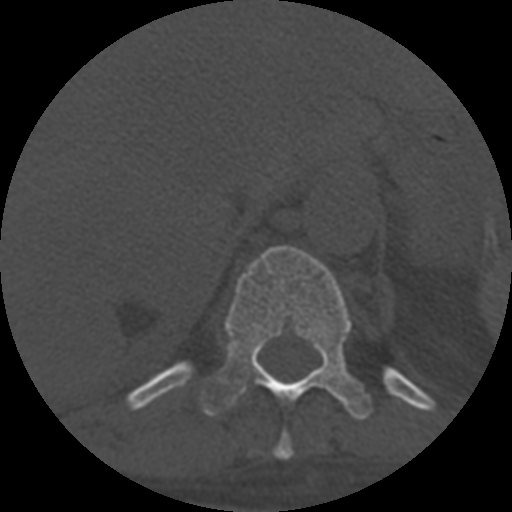
CT including the spine, one axial slice. Slice 339 of 708 in the series (ordered by position). Reconstruction kernel STANDARD. One of 3 acquisitions stored at this slice position. Bone window (W 1800 / L 400 HU). 1.25 mm slice thickness. 512 × 512 image matrix, field of view 160 × 160 mm. Patient age 55 years. Case-level facts recorded for this patient, not image findings: primary cancer: colon; vertebrae with lytic lesions (as recorded): T12, L1, L5.
Outlined on this slice (semi-automatically segmented with operator editing):
- T10 vertebra: box from (x=273, y=431) to (x=294, y=460) px
- T11 vertebra: (x=202, y=245)–(x=372, y=420)